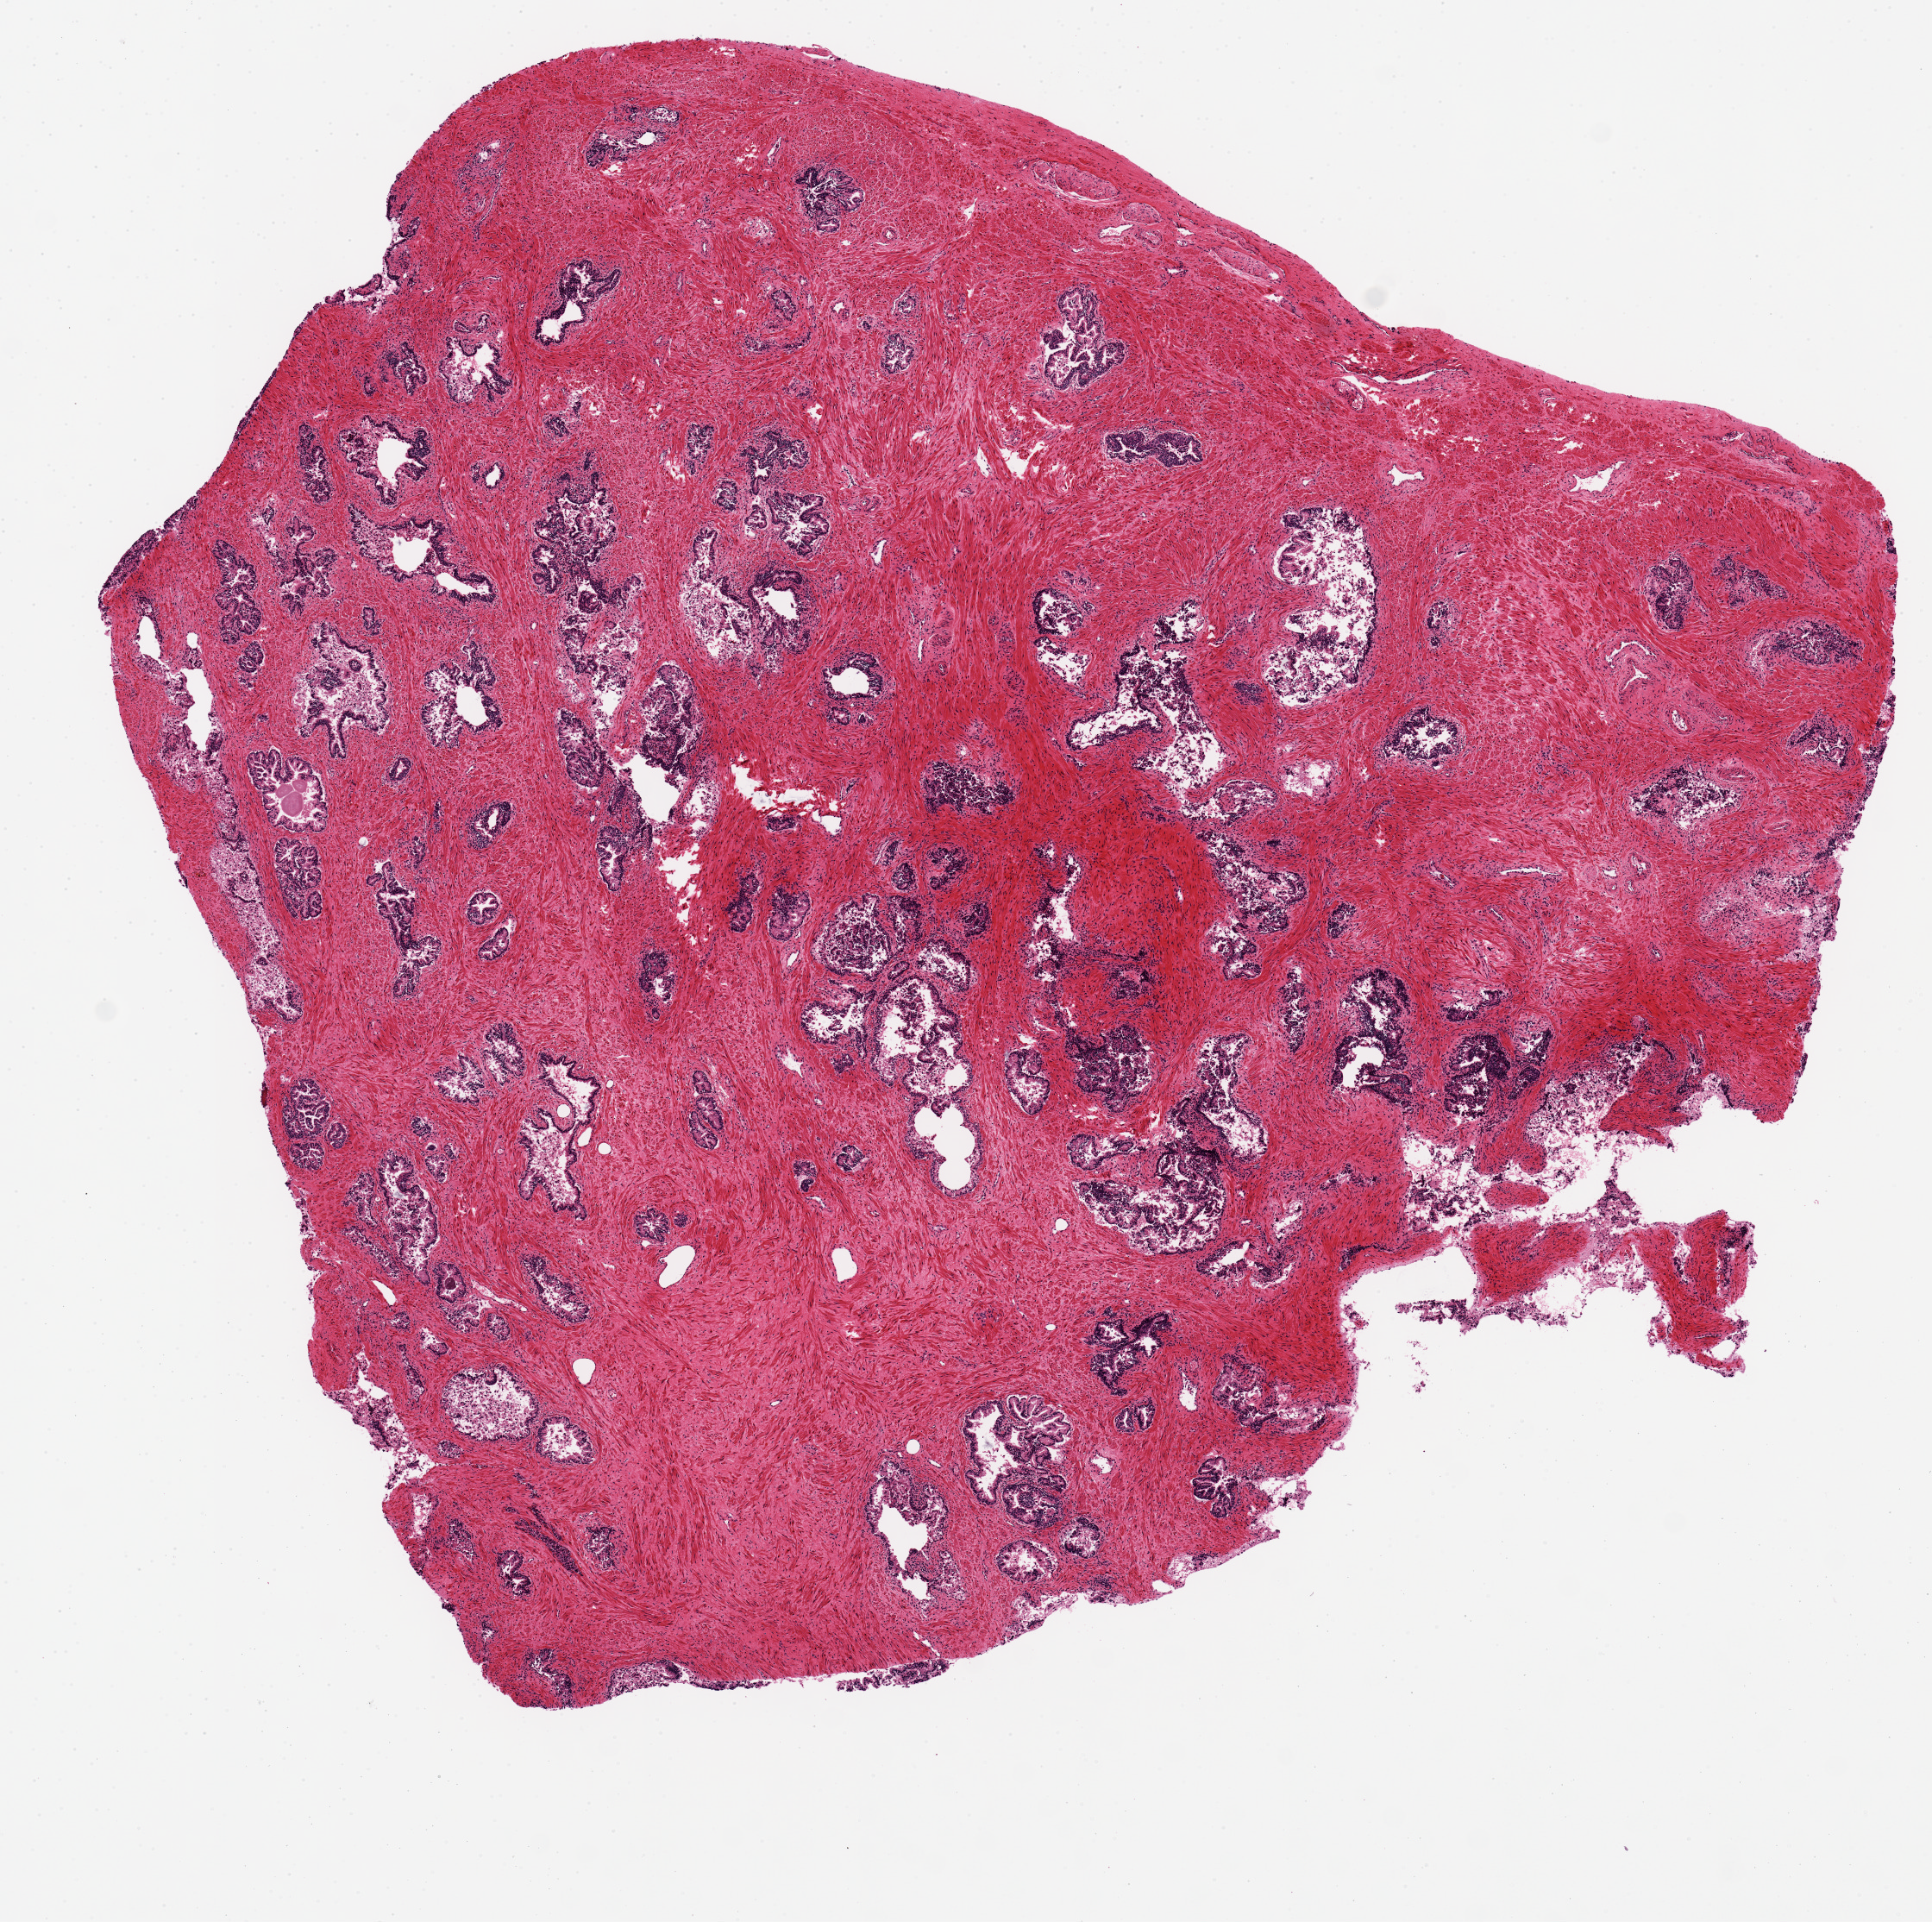
Whole-slide image, haematoxylin and eosin stain, shown as a low-resolution overview of the whole scanned area (about 8.9 x 8.8 mm), PAXgene-fixed paraffin-embedded (PFPE) section, target tissue: prostate, donor tissue sample. Donor: male.
* reviewer comment on this tissue sample: 8x7.4mm. Glandular hyperplasia